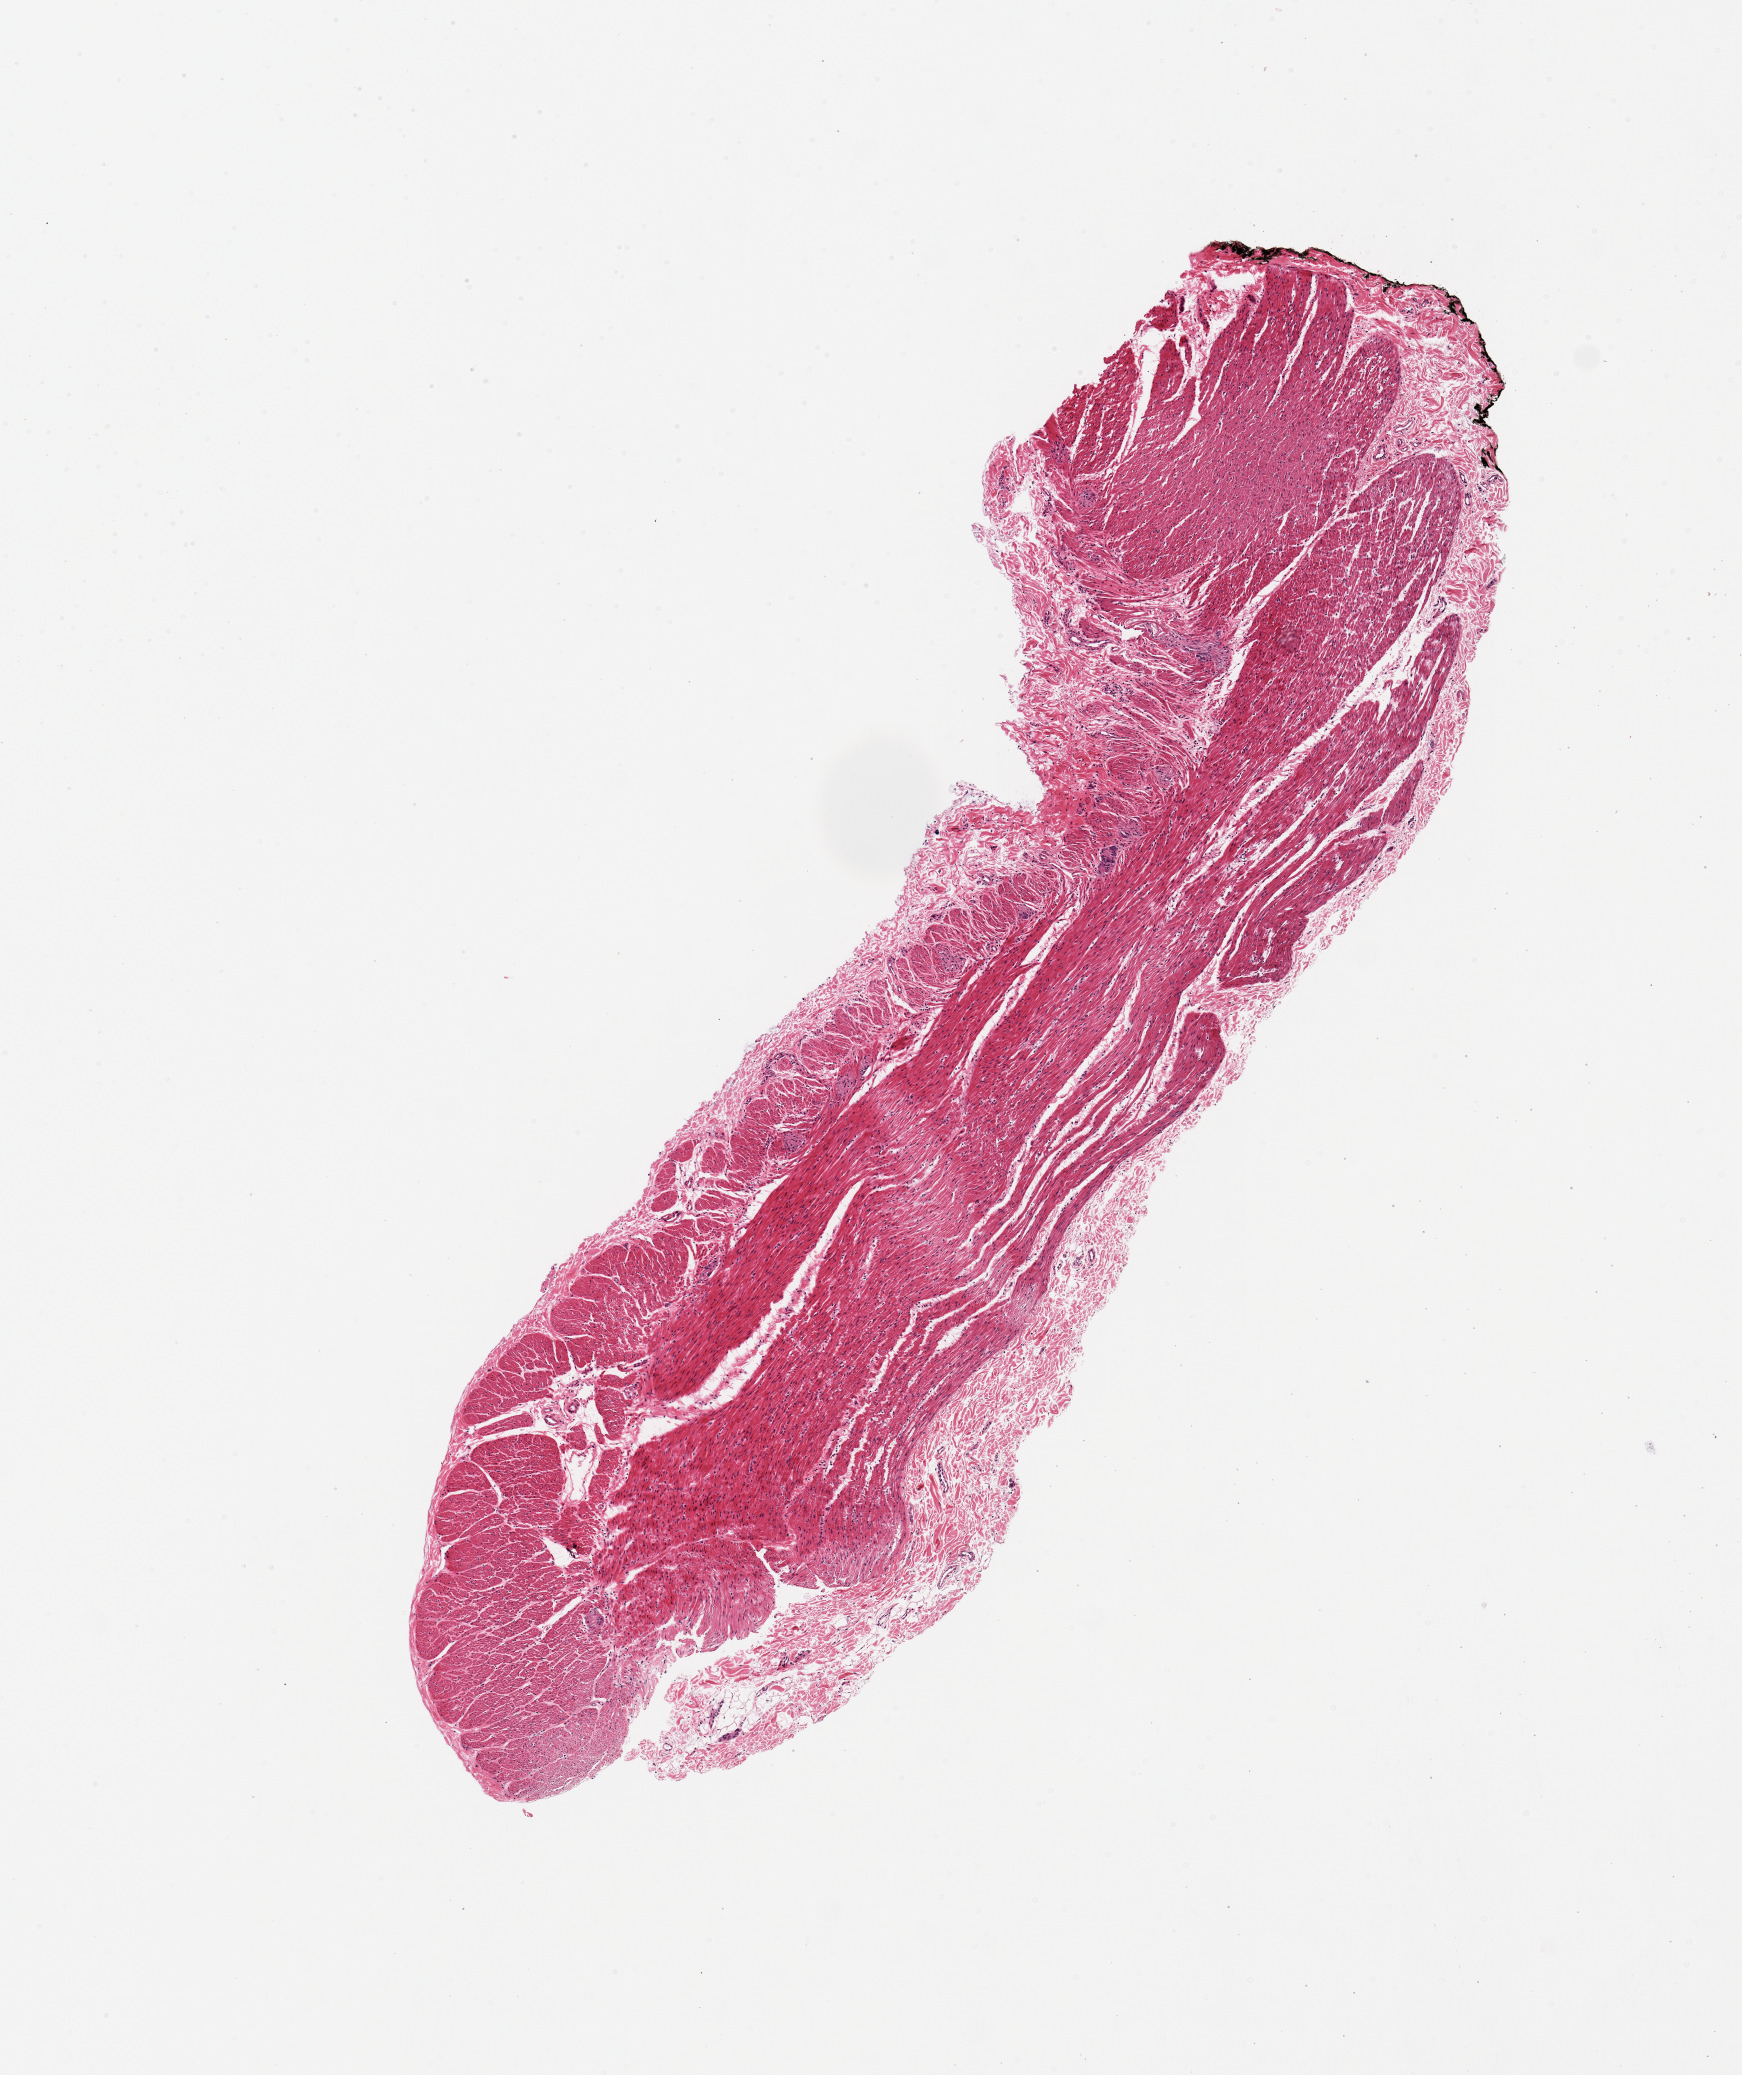
Whole-slide image, H&E stain, a low-resolution overview of the entire scanned area, about 6.9 x 8.2 mm (from a 20x scan). PAXgene-fixed, paraffin-embedded tissue. Target tissue: transverse colon. Donor tissue sample. Donor sex: female.
Pathologist's review note for this sample: 1 piece, 7x2mm; all muscularis; no mucosa.